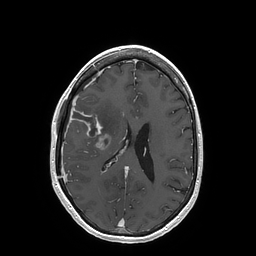
Brain MRI from a brain-tumour surgery series, one axial slice; slice 70 of 202 in the series (ordered by position); T1-weighted post-contrast; 1 mm slice thickness; 256 × 256 image matrix, field of view 250 × 250 mm. From the clinical record (not read from this slice): histopathology: Glioblastoma; WHO grade: 4; IDH mutation: no; tumour location: Right Insular.
Annotated regions visible in this slice (expert manual segmentation):
- tumour: bounding box [x1, y1, x2, y2] px = [70, 108, 110, 150]